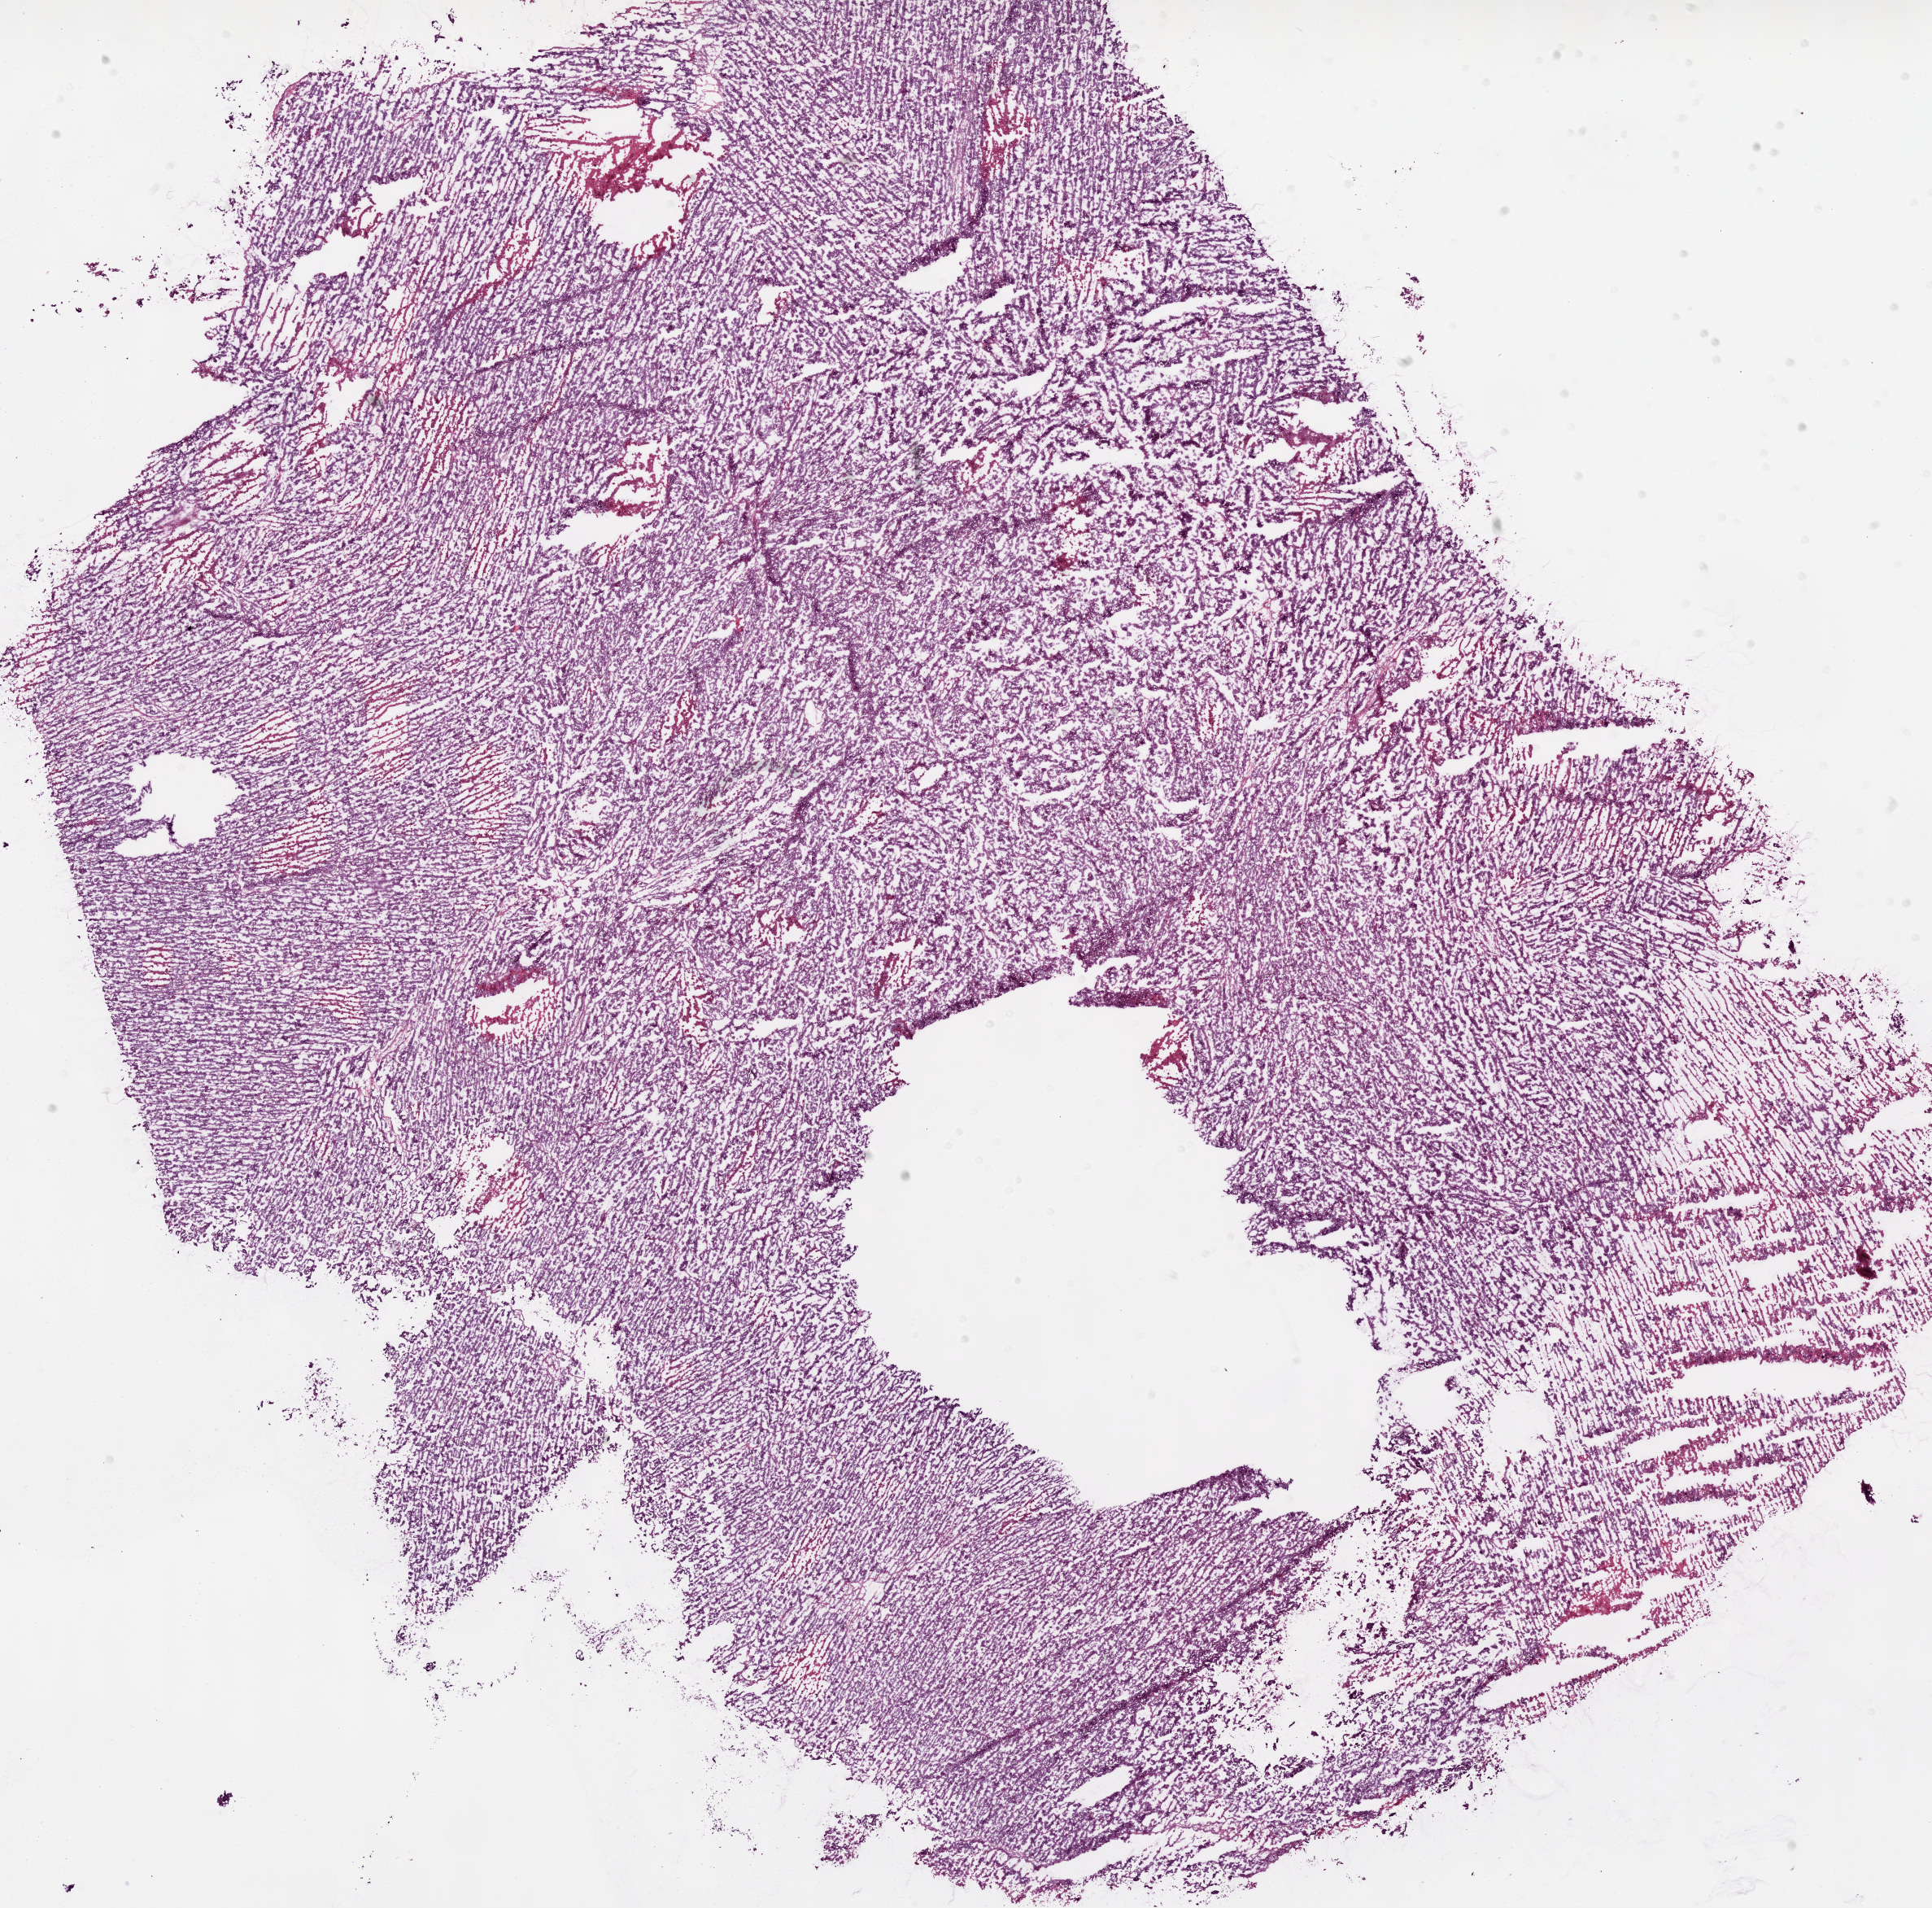
Digitized Hematoxylin and eosin (H&E) stained tissue section (whole slide) — low-resolution overview of the scanned area, about 19.1 x 18.8 mm; frozen section from the bottom of the tissue portion; primary tumour sample from the ovary. Female, age 49 years at initial diagnosis. Histologic grade: G3 (poorly differentiated). Pathologist review of this section (percent, as recorded): tumour cells 89%, tumour nuclei 99%, normal cells 0%, stromal cells 1%, necrosis 10%.
Pathologic diagnosis: Serous cystadenocarcinoma, NOS. FIGO stage: IIIC.